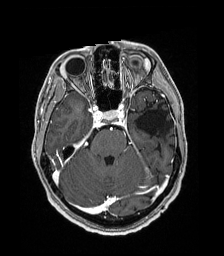
Brain MRI from a brain-tumour surgery series, one axial slice. Slice 122 of 192 in the series (ordered by position). T1-weighted post-contrast. 1 mm slice thickness. 224 × 256 image matrix, field of view 224 × 256 mm. From the clinical record (not read from this slice): histopathology: Low grade glioma; IDH mutation: no; tumour location: Left Parieto-Occipital Intraventricular.
Annotated regions visible in this slice (expert manual segmentation):
- previous resection cavity: bounding box <135,104,167,137> (left, top, right, bottom; pixels)